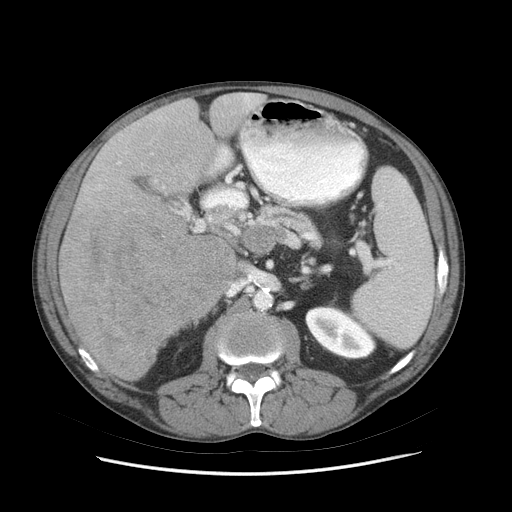
Contrast-enhanced abdominal CT (liver protocol), one axial slice; position 36 of 89 along the scan axis; reconstruction kernel STANDARD; soft-tissue window (W 400 / L 40 HU); 2.5 mm slice thickness; 512 × 512 image matrix, field of view 380 × 380 mm. Case-level facts recorded for this patient, not image findings: diagnosis: hepatocellular carcinoma (patient treated with transarterial chemoembolisation; whether this scan precedes or follows treatment is not stated here); TNM stage (as recorded): Stage-IIIB.
Outlined on this slice (semi-automatic segmentation, software-assisted and operator-edited):
- liver parenchyma outside the tumour (the mass and vessels are separate outlines, so this box may not span the whole liver): box from (x=58, y=92) to (x=264, y=380) px
- mass: (x=60, y=206)–(x=235, y=380)
- liver vessels: (x=118, y=94)–(x=253, y=221)